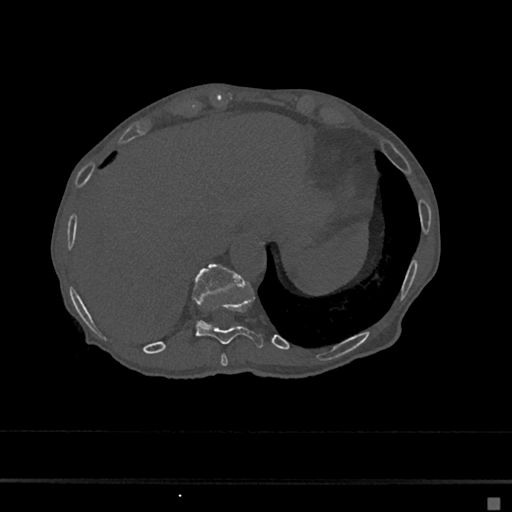
CT including the spine, one axial slice; slice 214 of 797 in the series (ordered by position); 120 kVp; bone window (W 1800 / L 400 HU); 512 × 512 image matrix. Patient: female, 68 years. Case-level facts recorded for this patient, not image findings: primary cancer: renal.
Annotated regions visible in this slice (semi-automatic segmentation, software-assisted and operator-edited):
- T10 vertebra: bounding box (x1, y1, x2, y2) in pixels: (196, 298, 264, 348)
- T11 vertebra: (193, 263, 246, 326)
- T9 vertebra: (220, 354, 228, 367)